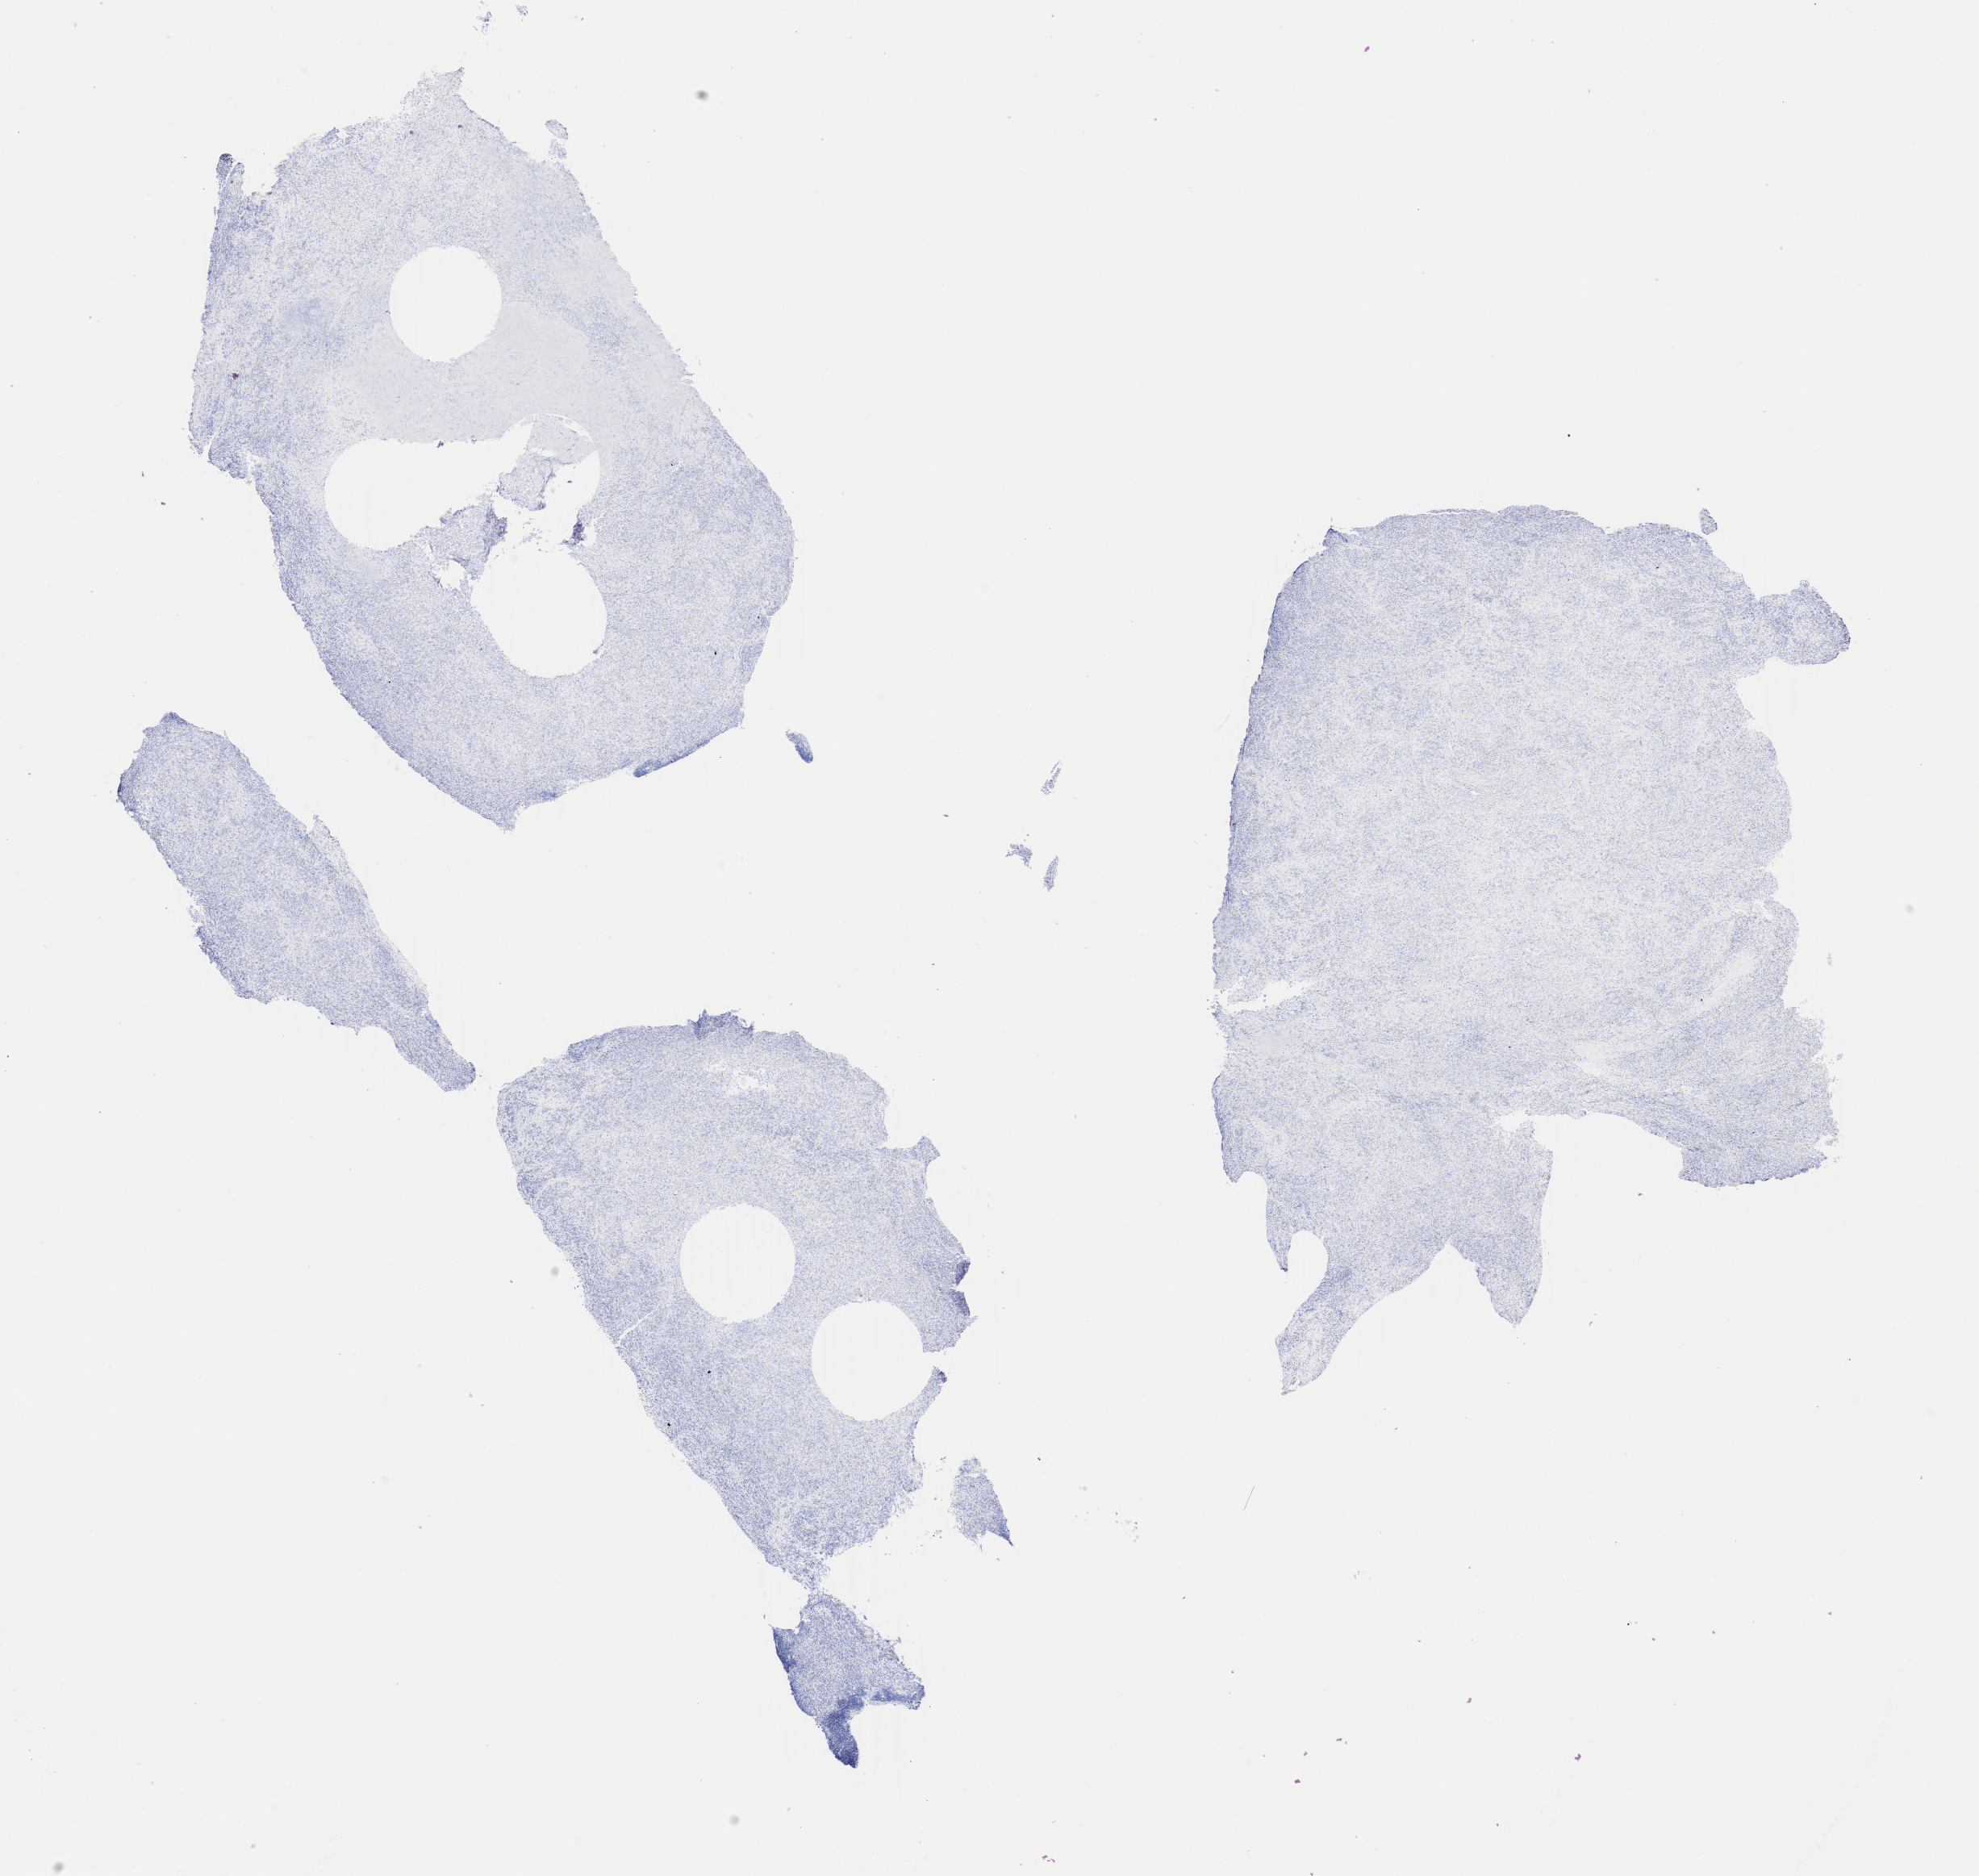
IHC for p40, whole-slide image — shown as a low-resolution overview of the whole scanned area (about 19.5 x 18.5 mm); specimen: tumor tissue; site: lung (left). Patient male; aged 65.
Histologic diagnosis: Carcinoma, undifferentiated, NOS.